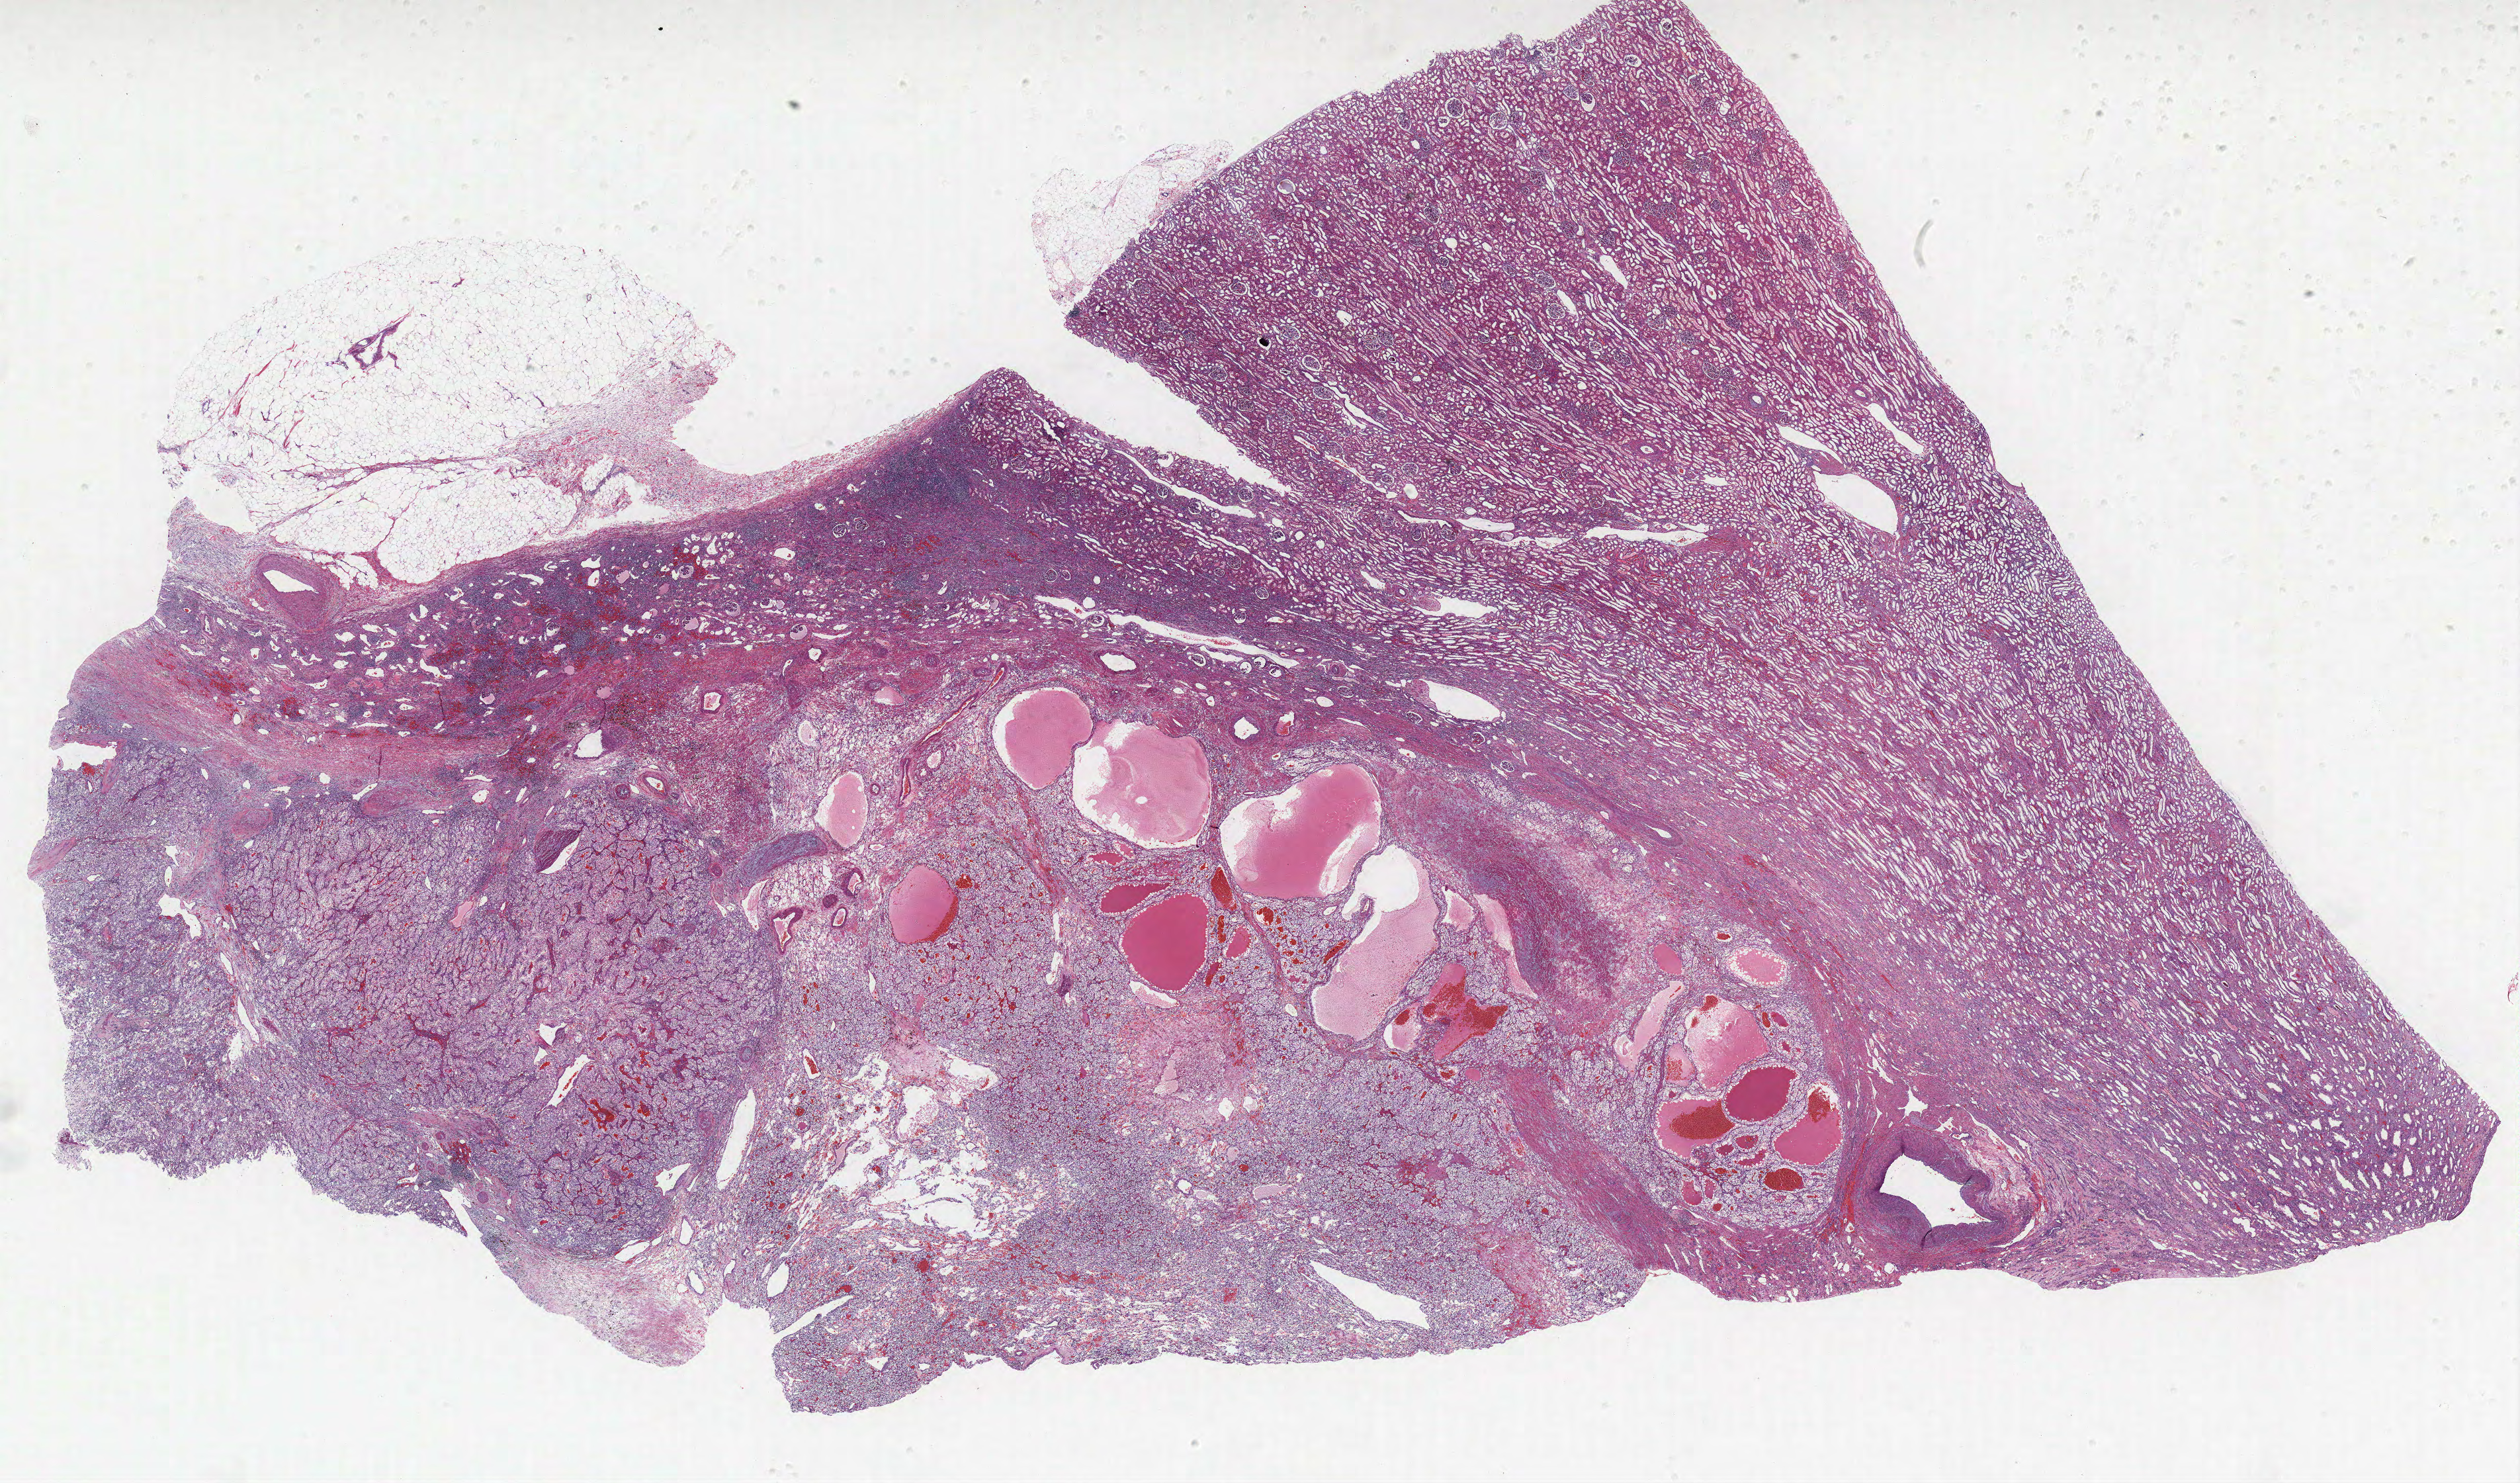
Hematoxylin and eosin (H&E) stained whole-slide image, a low-resolution overview of the entire scanned area, about 30.4 x 17.9 mm (from a 40x scan), FFPE section, primary tumour sample from the kidney. Patient: male, age at initial diagnosis 64 years.
Histologic diagnosis: Clear cell adenocarcinoma, NOS.